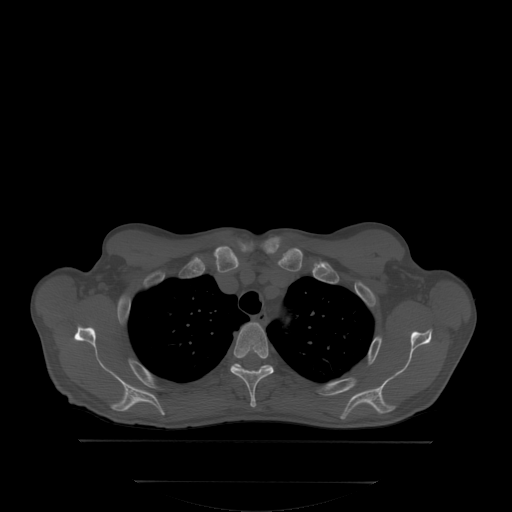
CT including the spine, one axial slice. Bone window (W 1800 / L 400 HU). 2.5 mm slice thickness. 512 × 512 image matrix, field of view 500 × 500 mm. Male patient, age 58 years. Case-level facts recorded for this patient, not image findings: primary cancer: prostate.
Annotated regions visible in this slice (semi-automatically segmented with operator editing):
- T3 vertebra: bounding box <230,323,274,406> (left, top, right, bottom; pixels)
- T4 vertebra: <238,365,271,369>